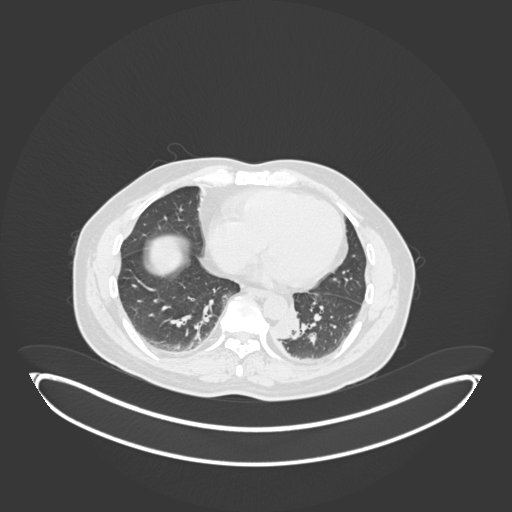
Chest CT, one axial slice. Slice 57 of 258 in the series (ordered by position). Reconstruction kernel B30f. Lung window (W 1500 / L -600 HU). 1 mm slice thickness. 512 × 512 image matrix, field of view 500 × 500 mm. Male patient, age 54 years. From the clinical record (not read from this slice): clinical TNM (as recorded): T3 N0 M0.
Outlined on this slice (bounding box drawn by a radiologist):
- lung tumour (recorded histology: squamous cell carcinoma): box from (x=270, y=301) to (x=305, y=344) px